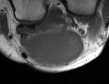
MRI of an extremity soft-tissue mass, one axial slice; slice 17 of 50 in the series (ordered by position); MR volume resampled by the dataset authors to the PET/CT grid (not the native acquisition matrix); 3.27 mm slice thickness; 109 × 84 image matrix, field of view 106 × 82 mm. Male patient. Case-level facts recorded for this patient, not image findings: histological type: synovial sarcoma; site of the primary tumour: left poplietal fossa.
Outlined on this slice (expert contour drawn on MRI and transferred to this co-registered scan by the dataset authors):
- gross tumour volume (mass): bounding box (x1, y1, x2, y2) in pixels: (20, 28, 83, 67)